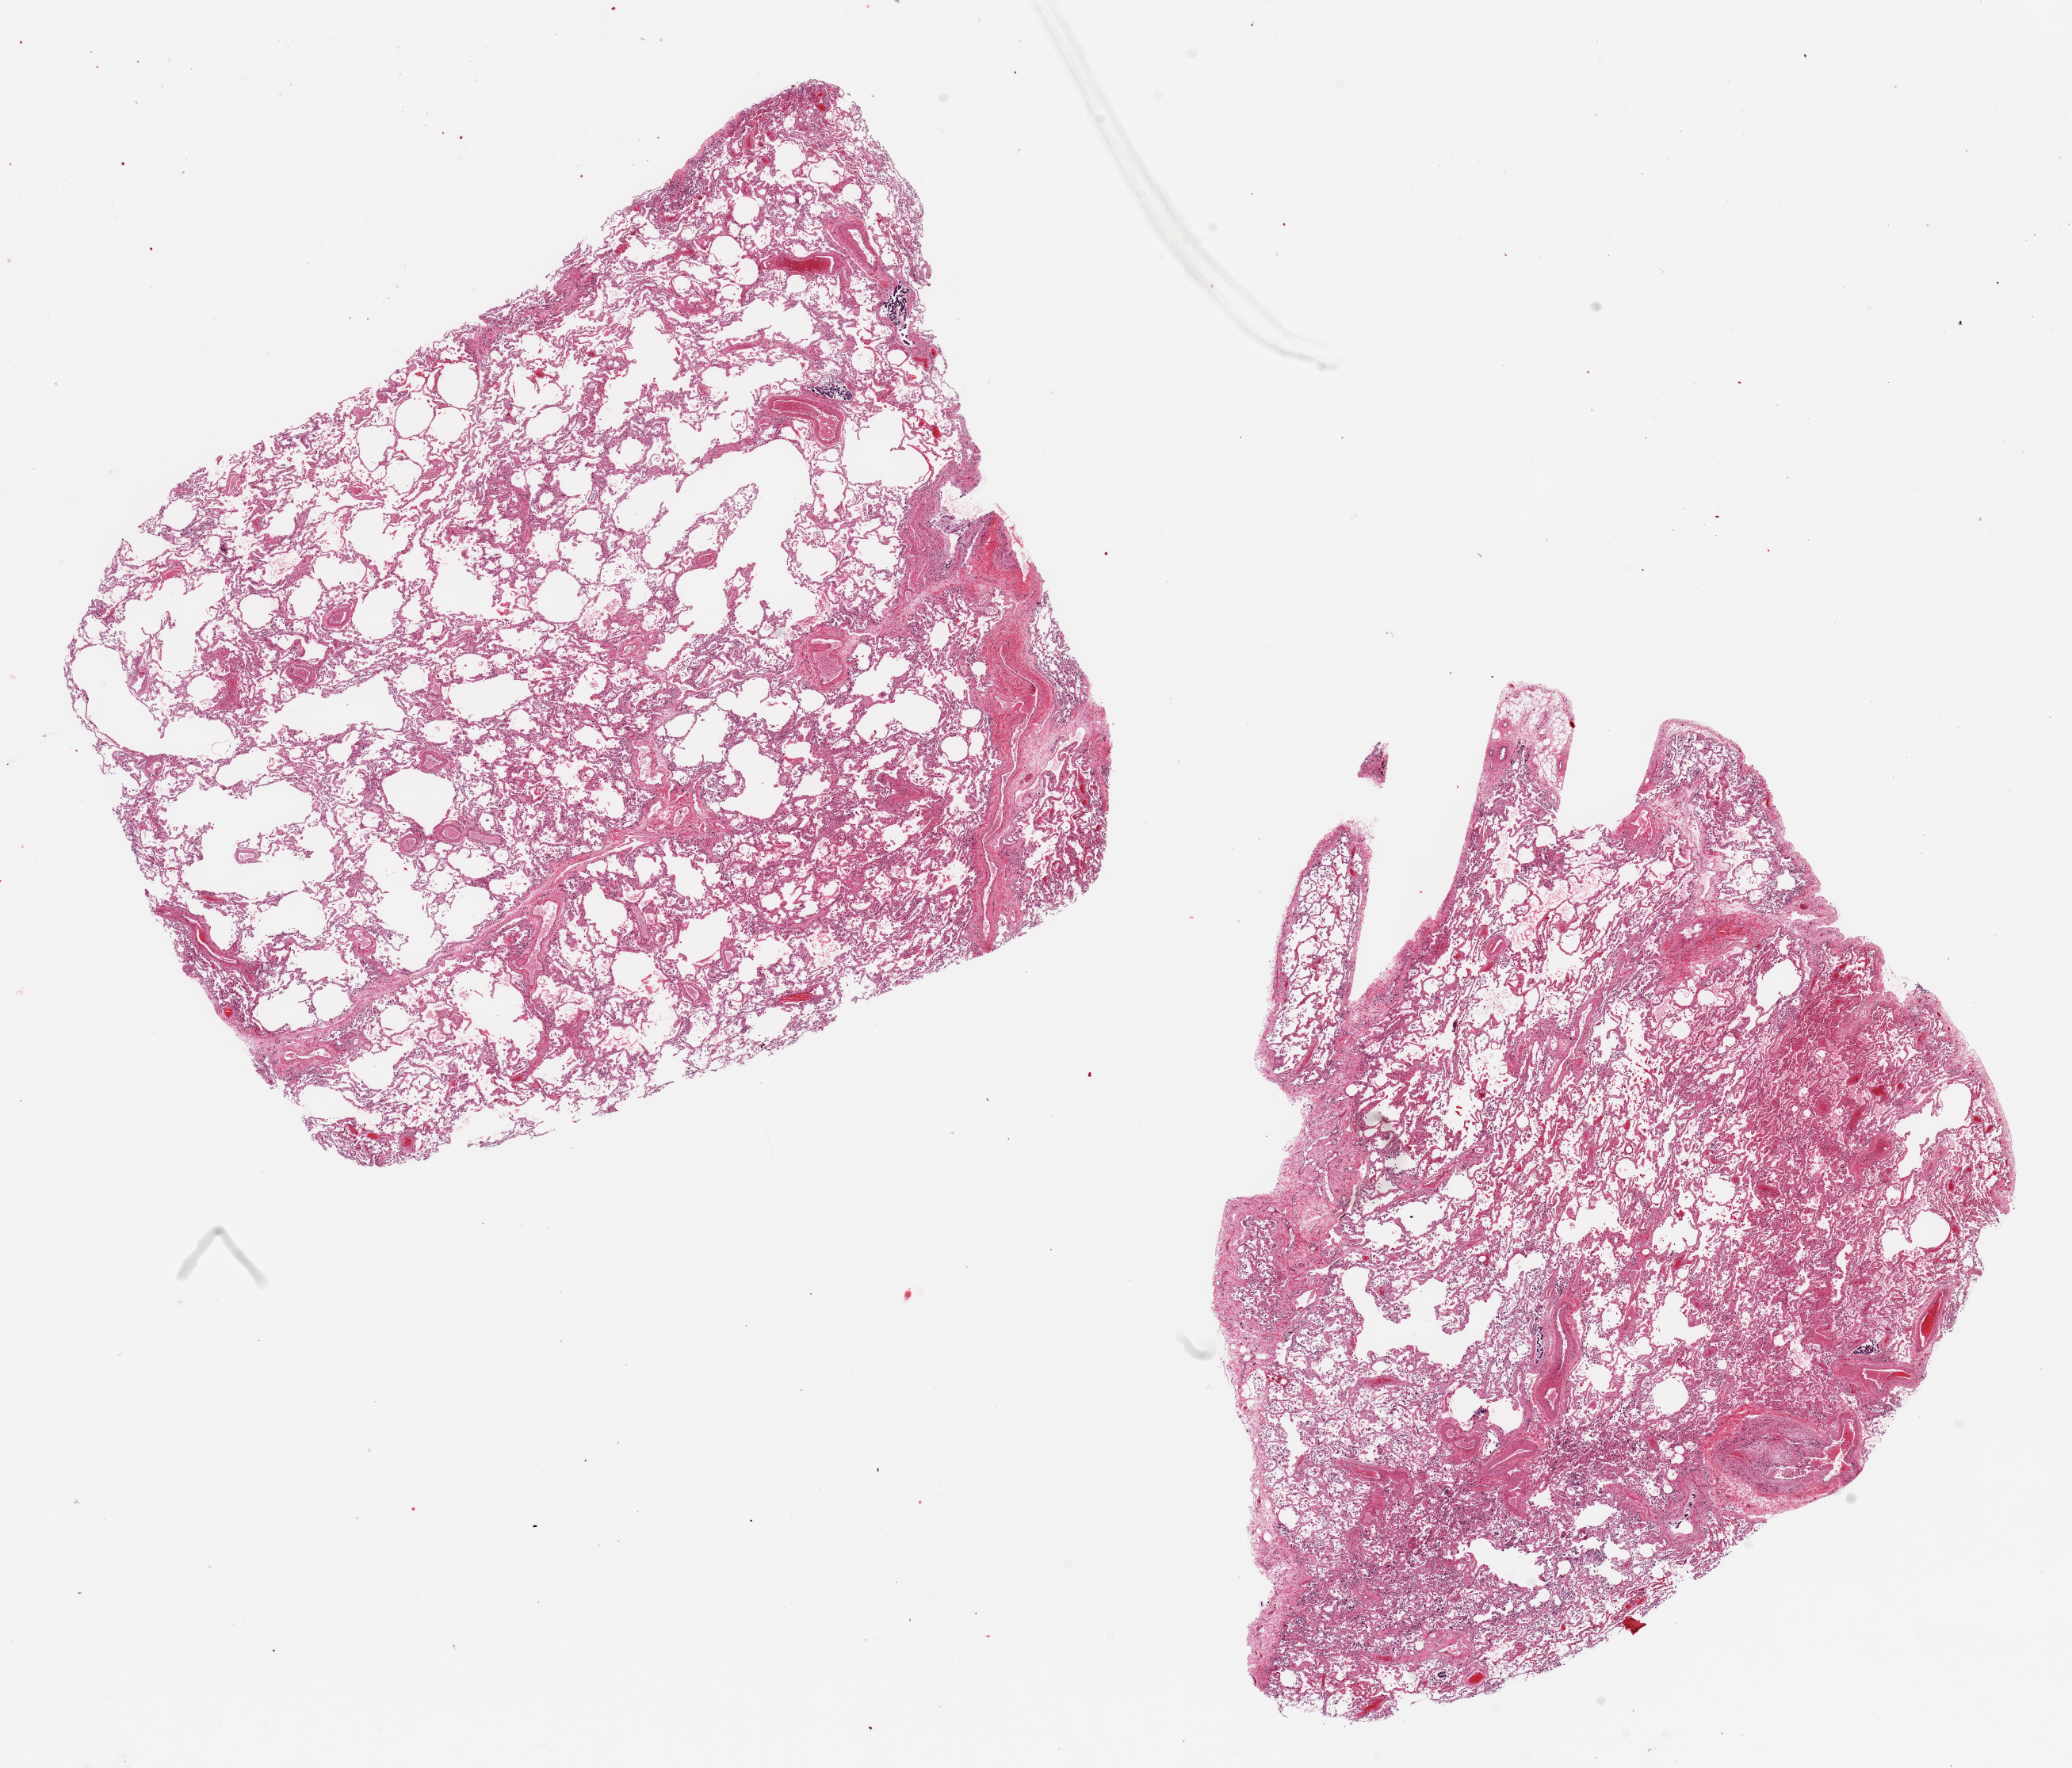
Digitized hematoxylin and eosin (H&E)-stained section, a low-resolution overview of the entire scanned area, about 20.7 x 17.6 mm (acquisition: 20x scan), PAXgene-fixed paraffin-embedded (PFPE) section, target tissue: lung, tissue donor sample. Donor: male.
- review note (as recorded): 2 pieces, ~ 9.5x7.5mm ???at least one aliquot appears peripheral (contains fat)